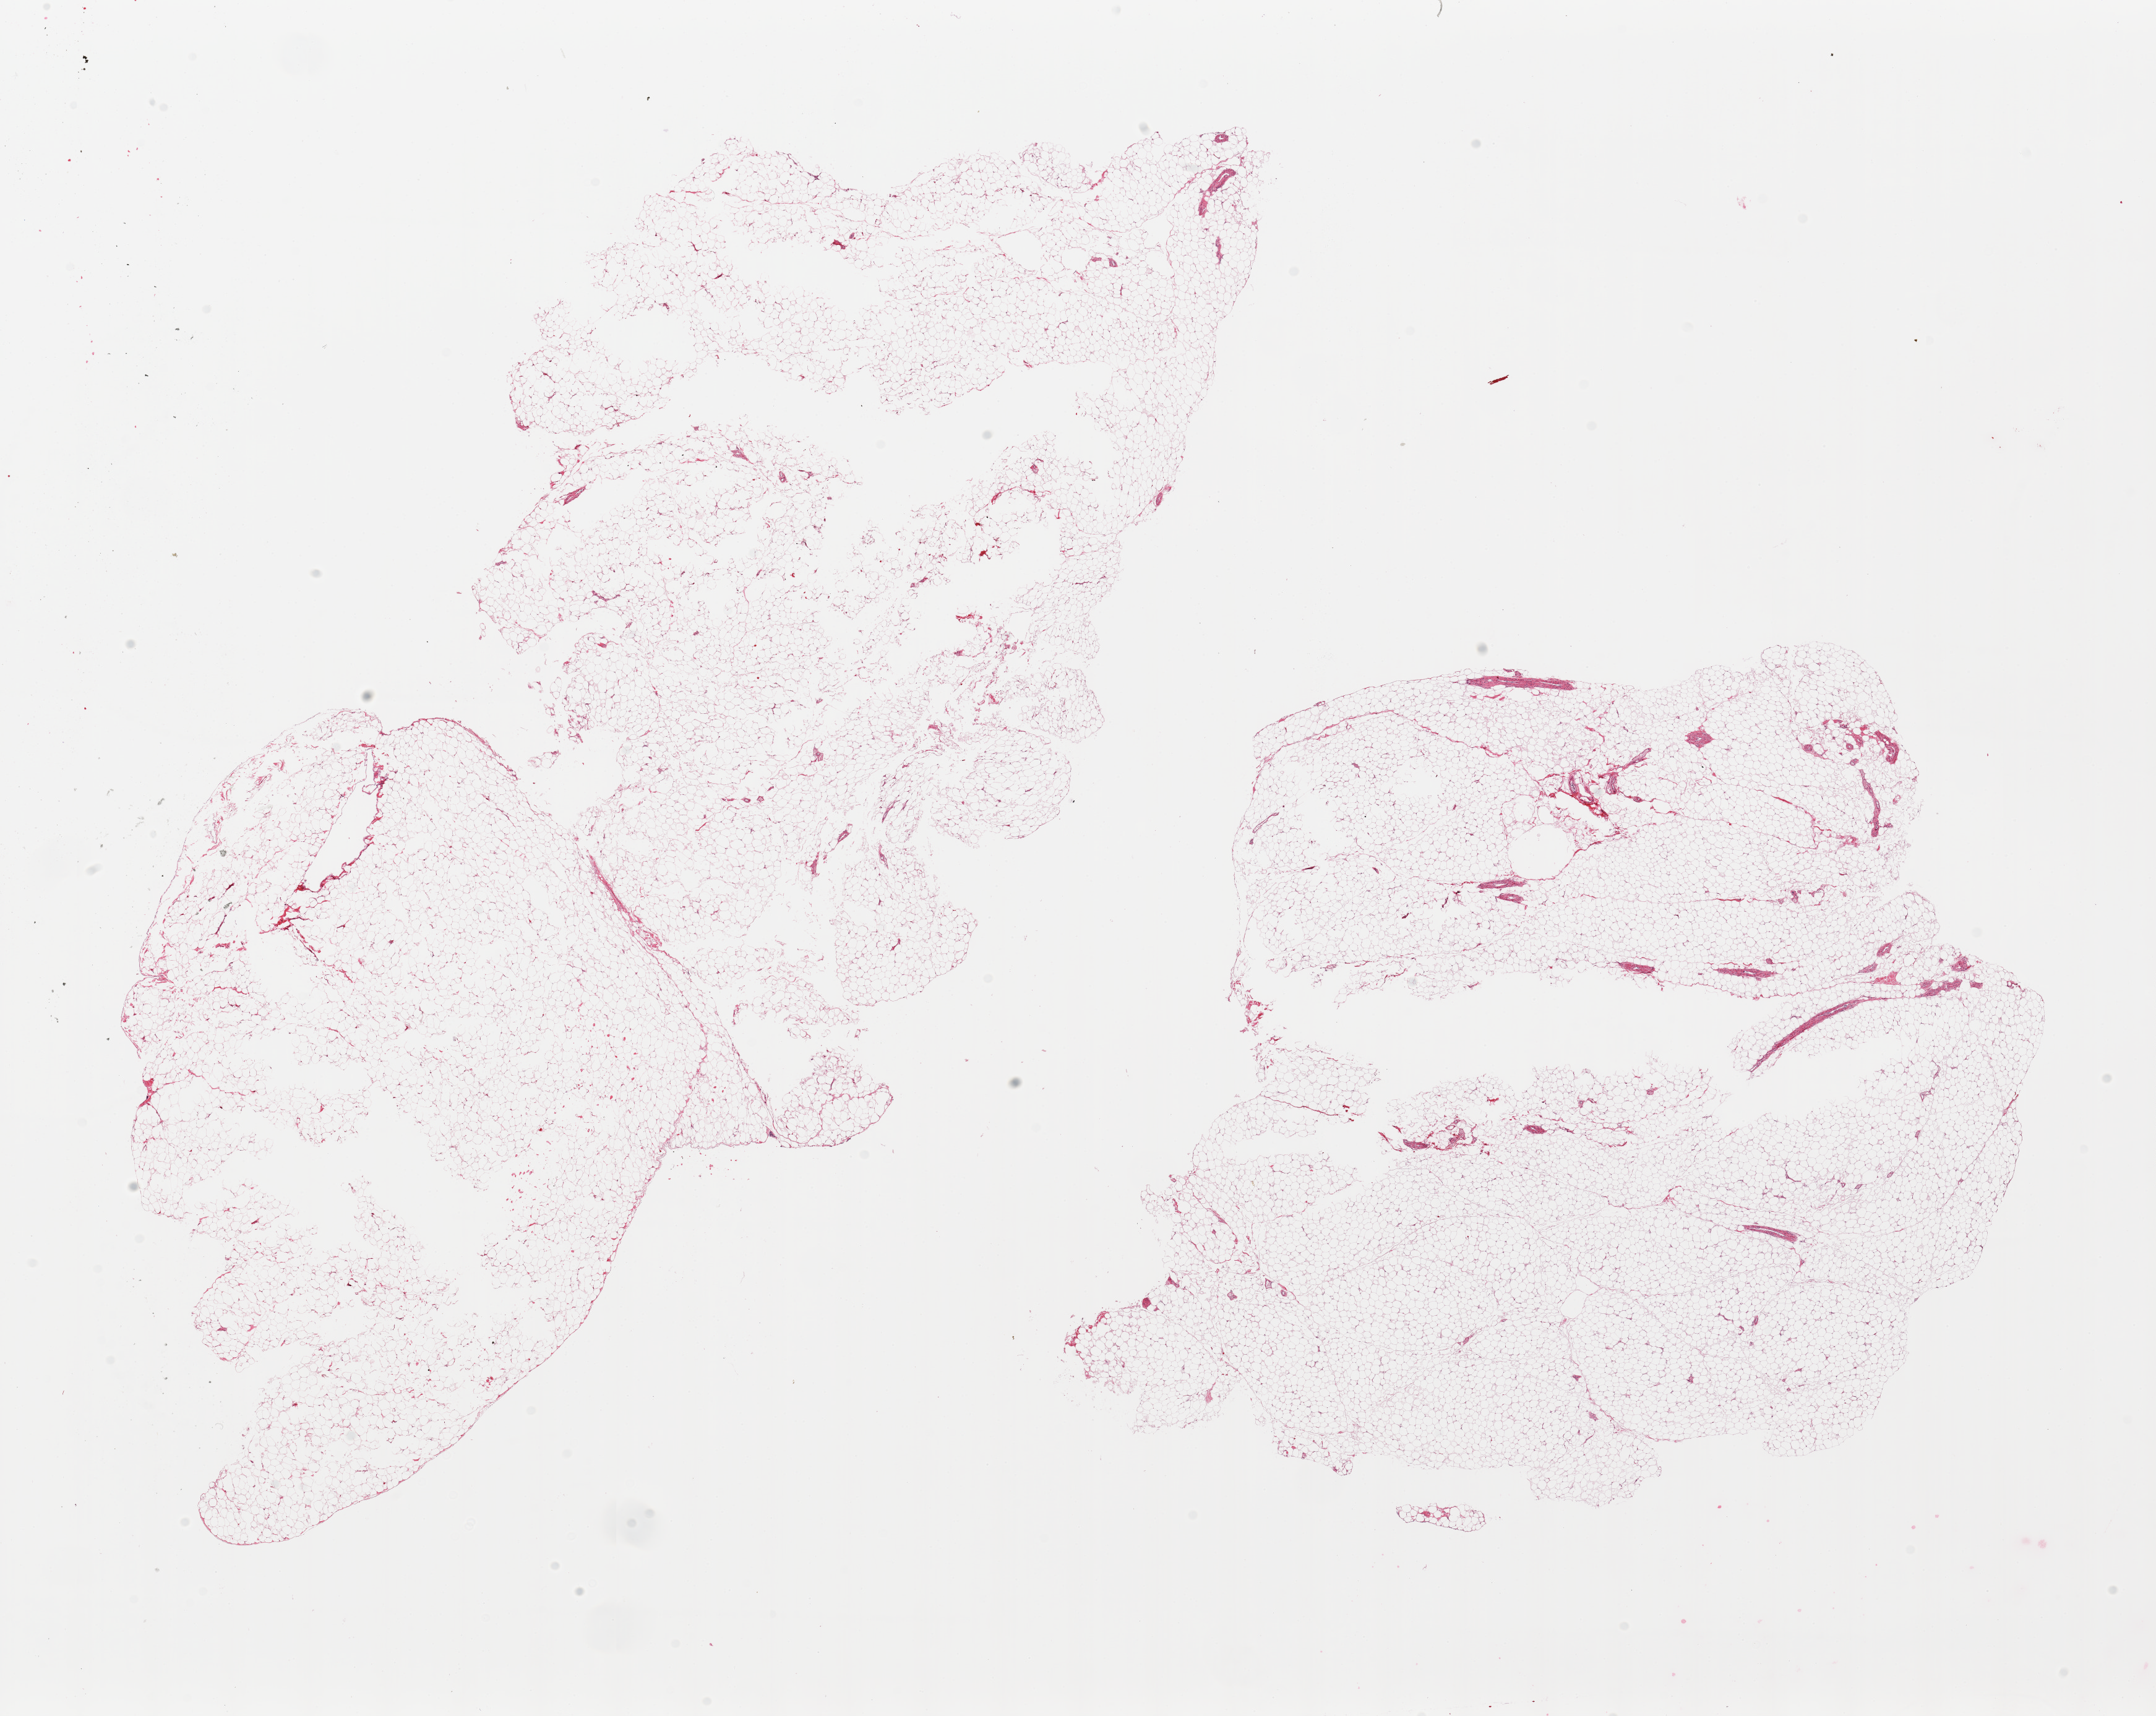
Digitized haematoxylin and eosin-stained section — a low-resolution overview of the entire scanned area, about 27.6 x 21.9 mm; PAXgene-fixed paraffin-embedded (PFPE) section; sampled site (target tissue): omentum; donor tissue sample.
Pathologist's review note for this sample: 2 pieces.